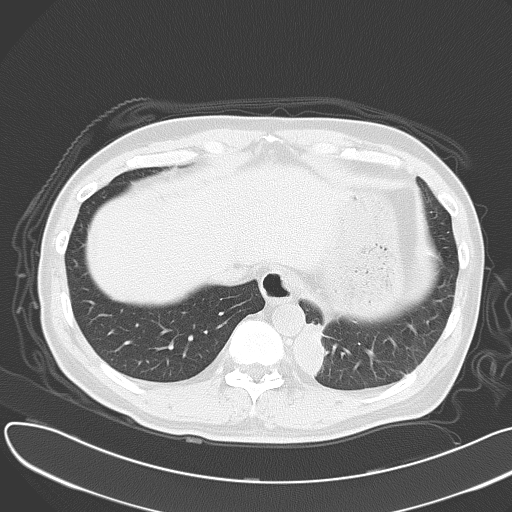
Chest CT, one axial slice; slice 10 of 55 in the series (ordered by position); 120 kVp; lung window (W 1500 / L -600 HU); 5 mm slice thickness; 512 × 512 image matrix. Patient: male, 55 years. From the clinical record (not read from this slice): clinical TNM (as recorded): T2 N3 M0; histopathological grade: G3.
Structures marked on this image (bounding box drawn by a radiologist):
- lung tumour (recorded histology: small cell carcinoma): box from (x=294, y=317) to (x=331, y=380) px